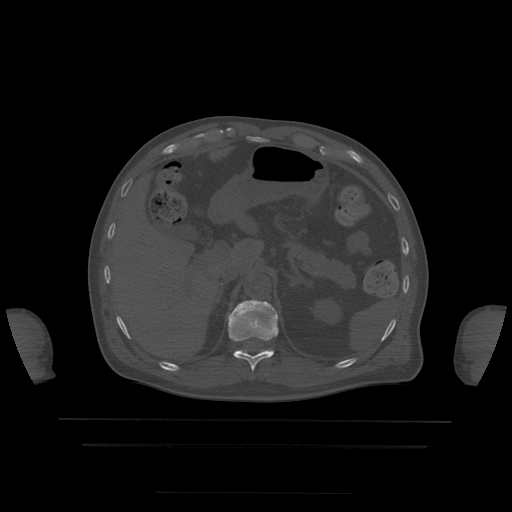
CT including the spine, one axial slice. Slice 214 of 522 in the series (ordered by position). Bone window (W 1800 / L 400 HU). 512 × 512 image matrix, field of view 436 × 436 mm. Patient age 68 years. Case-level facts recorded for this patient, not image findings: primary cancer: urothelial.
Structures marked on this image (semi-automatic segmentation, software-assisted and operator-edited):
- T11 vertebra: bounding box <228,300,279,372> (left, top, right, bottom; pixels)
- T12 vertebra: <242,351,246,353>